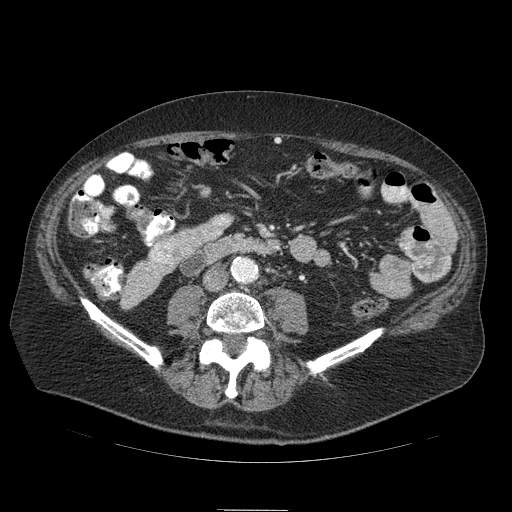
Contrast-enhanced abdominal CT (liver protocol), one axial slice; slice 8 of 103 in the series (ordered by position); 120 kVp; soft-tissue window (W 400 / L 40 HU); 2.5 mm slice thickness; 512 × 512 image matrix, field of view 440 × 440 mm. Case-level facts recorded for this patient, not image findings: diagnosis: hepatocellular carcinoma (patient treated with transarterial chemoembolisation; whether this scan precedes or follows treatment is not stated here); TNM stage (as recorded): Stage-IIIA; Child-Pugh class: B; tumour differentiation: well differentiated; tumour nodularity: multinodular.
Annotated regions visible in this slice (semi-automatically segmented with operator editing):
- mass: bounding box (x1, y1, x2, y2) in pixels: (150, 214, 231, 267)